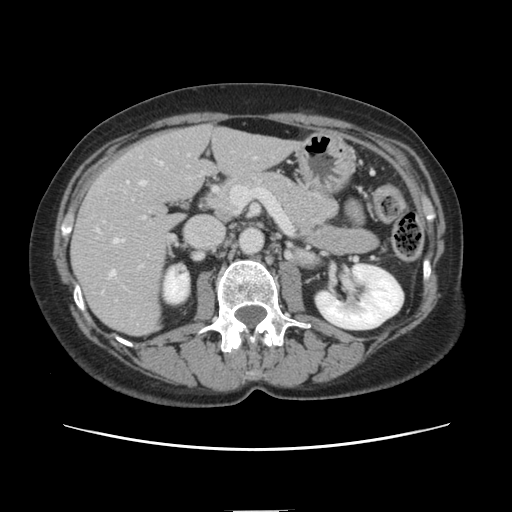
Contrast-enhanced abdominal CT, one axial slice; position 61 of 141 along the scan axis; 120 kVp; soft-tissue window (W 400 / L 40 HU); 2.5 mm slice thickness; 512 × 512 image matrix, field of view 350 × 350 mm. Female patient, age 63 years. Case-level facts recorded for this patient, not image findings: diagnosis: colorectal cancer liver metastases, imaged before liver resection; multiple liver metastases: yes; largest metastasis: 3.2 cm; disease in both lobes: yes.
Structures marked on this image (manually delineated by an expert):
- hepatic veins: bounding box <108,163,161,278> (left, top, right, bottom; pixels)
- liver: <72,126,295,335>
- planned liver remnant (the part of the liver to remain after resection): <176,126,295,189>
- portal vein (with intrahepatic branches): <116,180,143,244>